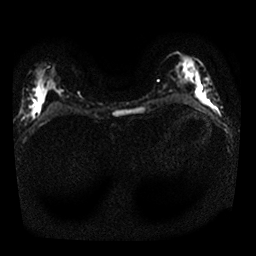
Breast MRI, one axial slice. Position 10 of 25 along the scan axis. Diffusion-weighted series; image 2 of 4 stored at this slice position (different b-values; order by instance number). 1.5 T. 256 × 256 image matrix. Female patient.
Outlined on this slice (manually delineated by an expert):
- tumour on diffusion-weighted imaging: bounding box [x1, y1, x2, y2] px = [195, 84, 210, 106]